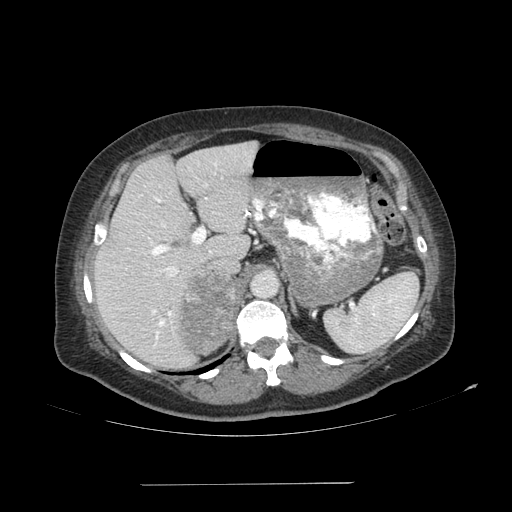
Contrast-enhanced abdominal CT, one axial slice. Position 71 of 113 along the scan axis. Reconstruction kernel SOFT. 120 kVp. Soft-tissue window (W 400 / L 40 HU). 2.5 mm slice thickness. 512 × 512 image matrix, field of view 440 × 440 mm. Female patient, age 67 years. Case-level facts recorded for this patient, not image findings: diagnosis: adrenocortical carcinoma; tumour side: right adrenal; tumour size at pathology: 9.8 cm; Ki-67 index: 59 %; stage (as recorded): 4.
Structures marked on this image (semi-automatically segmented with operator editing):
- mass: bounding box [x1, y1, x2, y2] px = [180, 273, 237, 352]